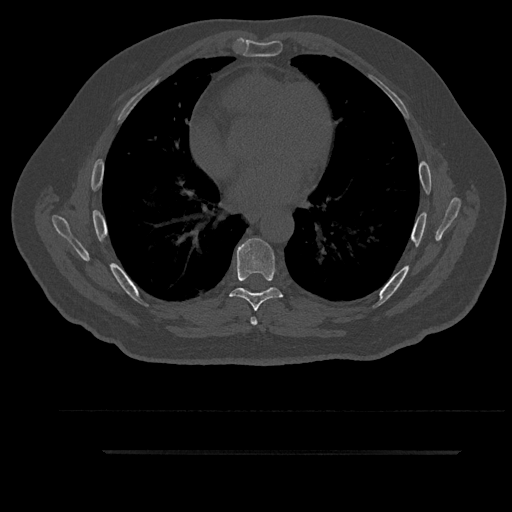
CT including the spine, one axial slice. Slice 528 of 797 in the series (ordered by position). Reconstruction kernel Br40s/3. Bone window (W 1800 / L 400 HU). 0.5 mm slice thickness. 512 × 512 image matrix. Male patient, age 63 years. Case-level facts recorded for this patient, not image findings: primary cancer: renal; vertebrae with lytic lesions (as recorded): T8.
Structures marked on this image (semi-automatically segmented with operator editing):
- T6 vertebra: bounding box <251,288,270,325> (left, top, right, bottom; pixels)
- T7 vertebra: <229,238,283,311>